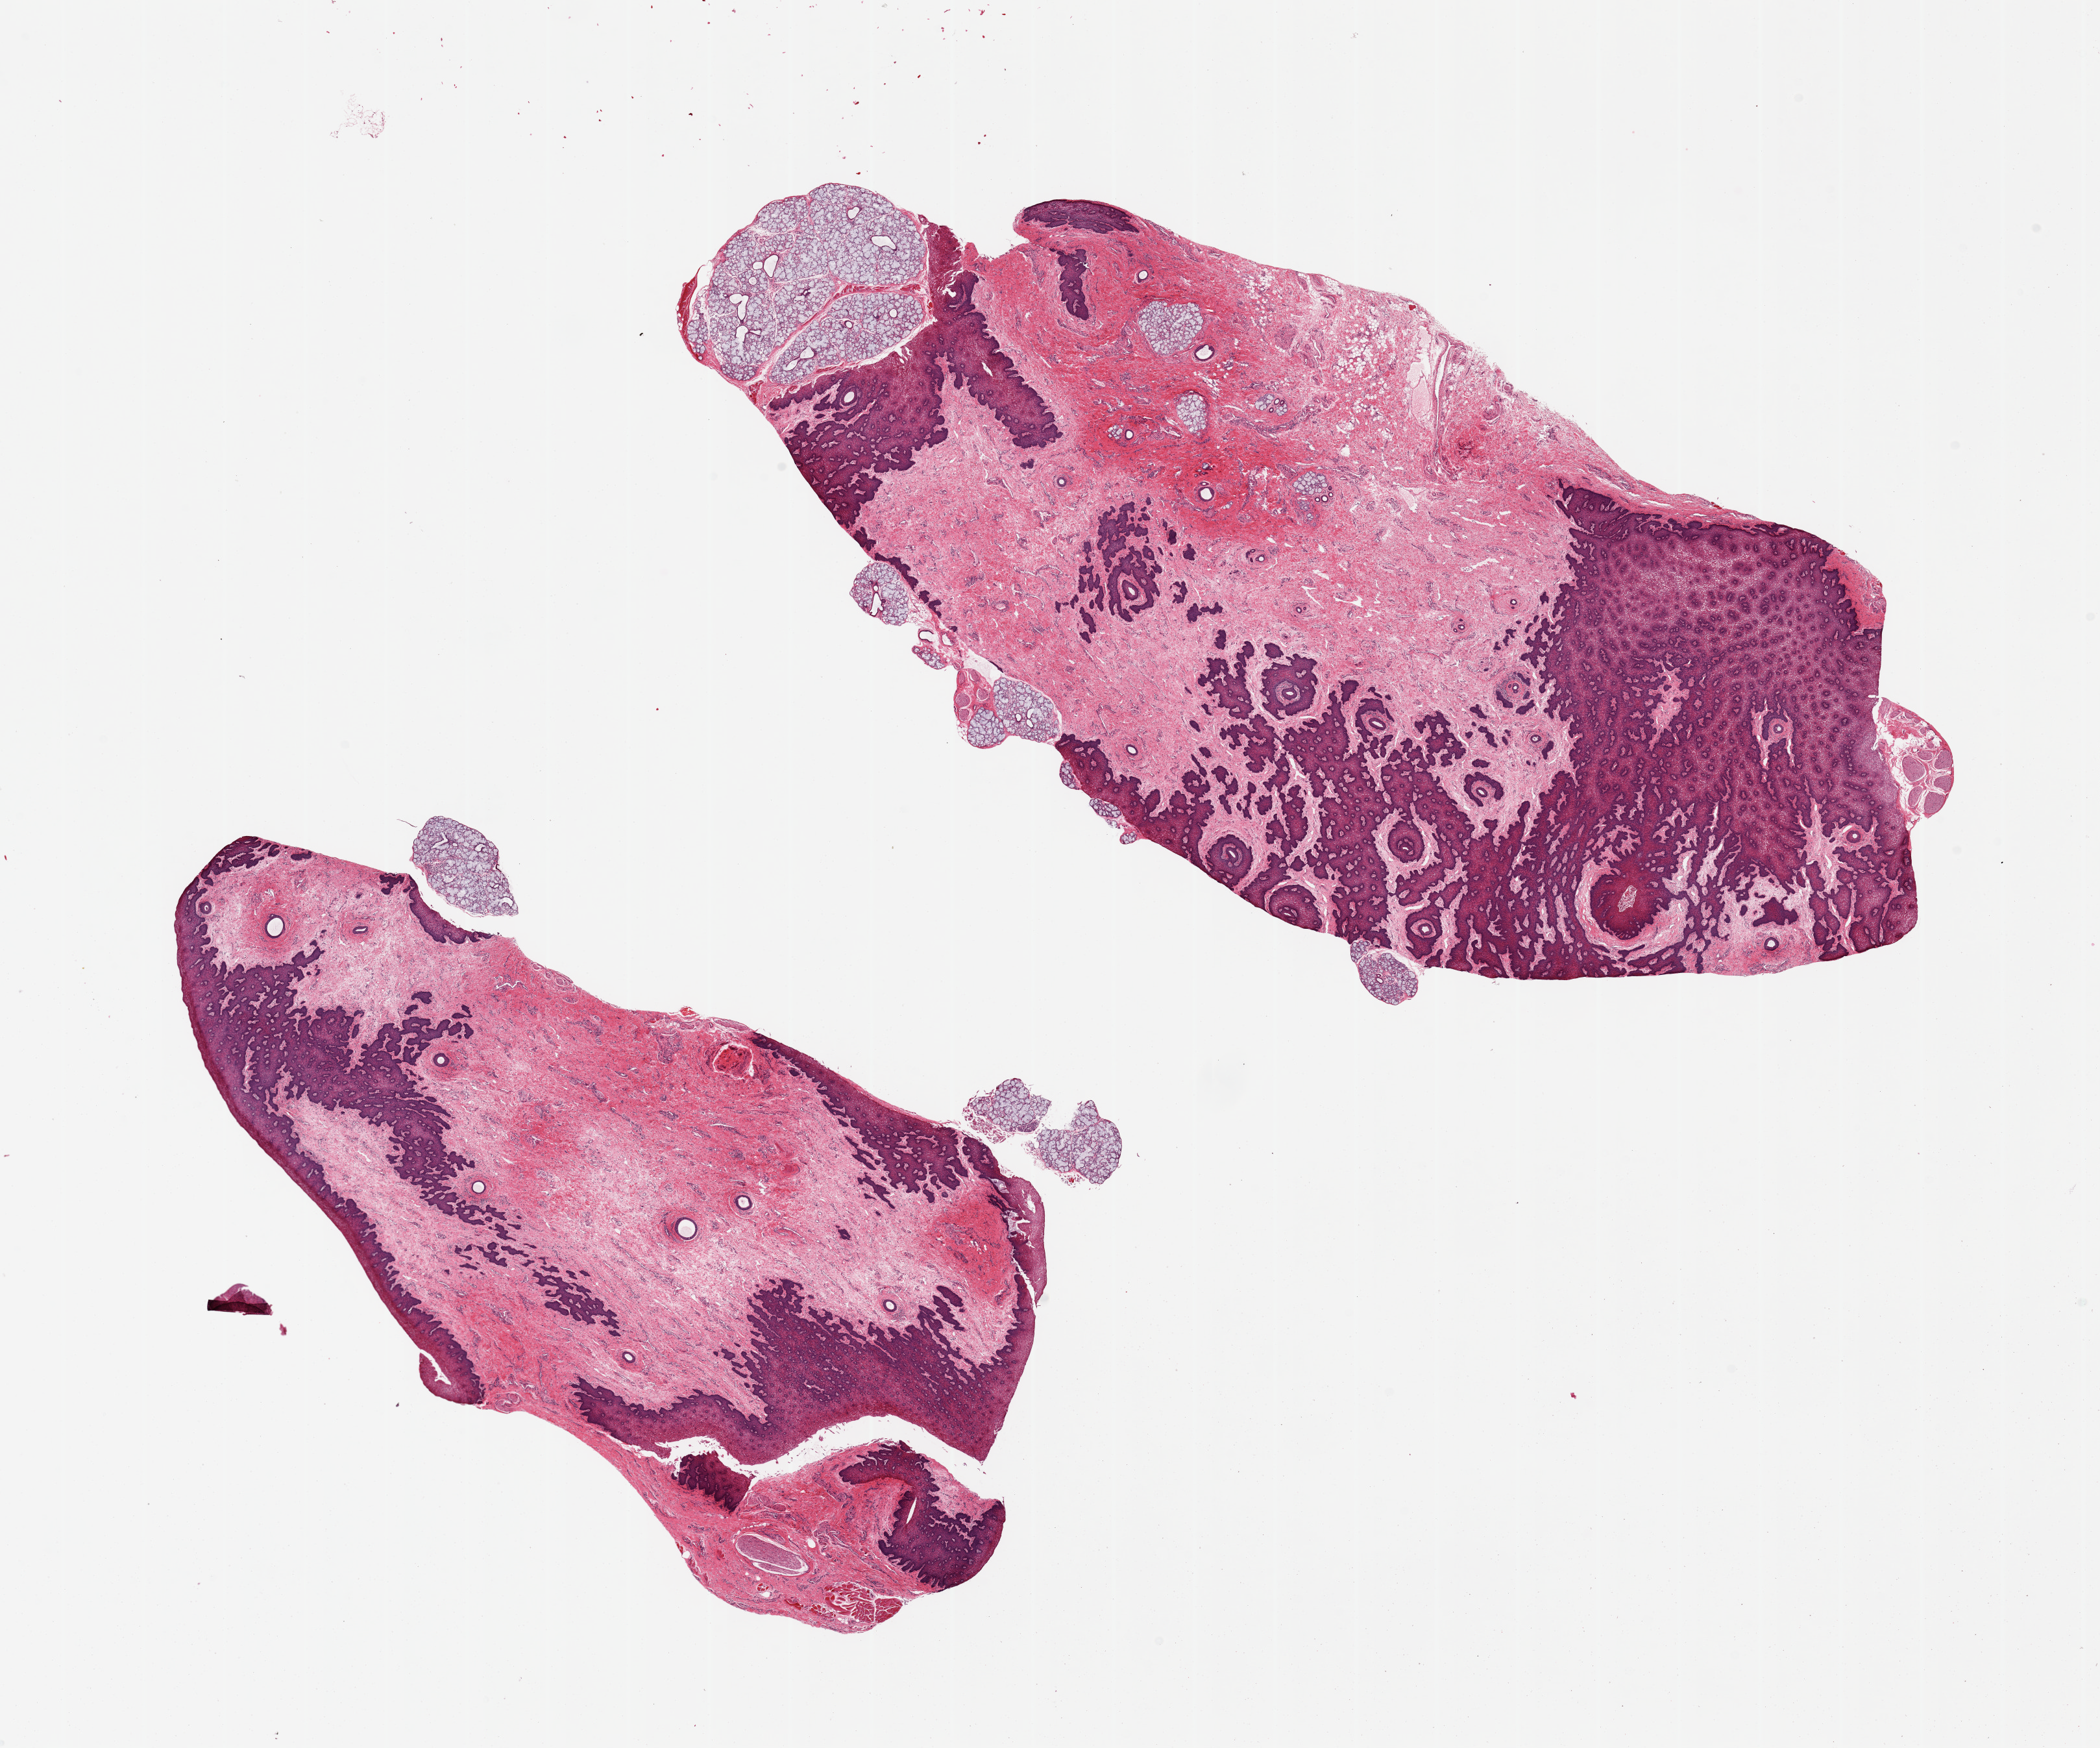
Digitized hematoxylin and eosin (H&E)-stained section — a low-resolution overview of the entire scanned area, about 25.6 x 21.3 mm; PAXgene-fixed, paraffin-embedded tissue; sampled site (target tissue): minor salivary gland; tissue donor sample. Donor sex: female.
• pathologist's review note for this sample: 2 pieces fragments of glandular tissue range from 1-3mm; ~10% of specimen; rest squamous mucosa/stroma